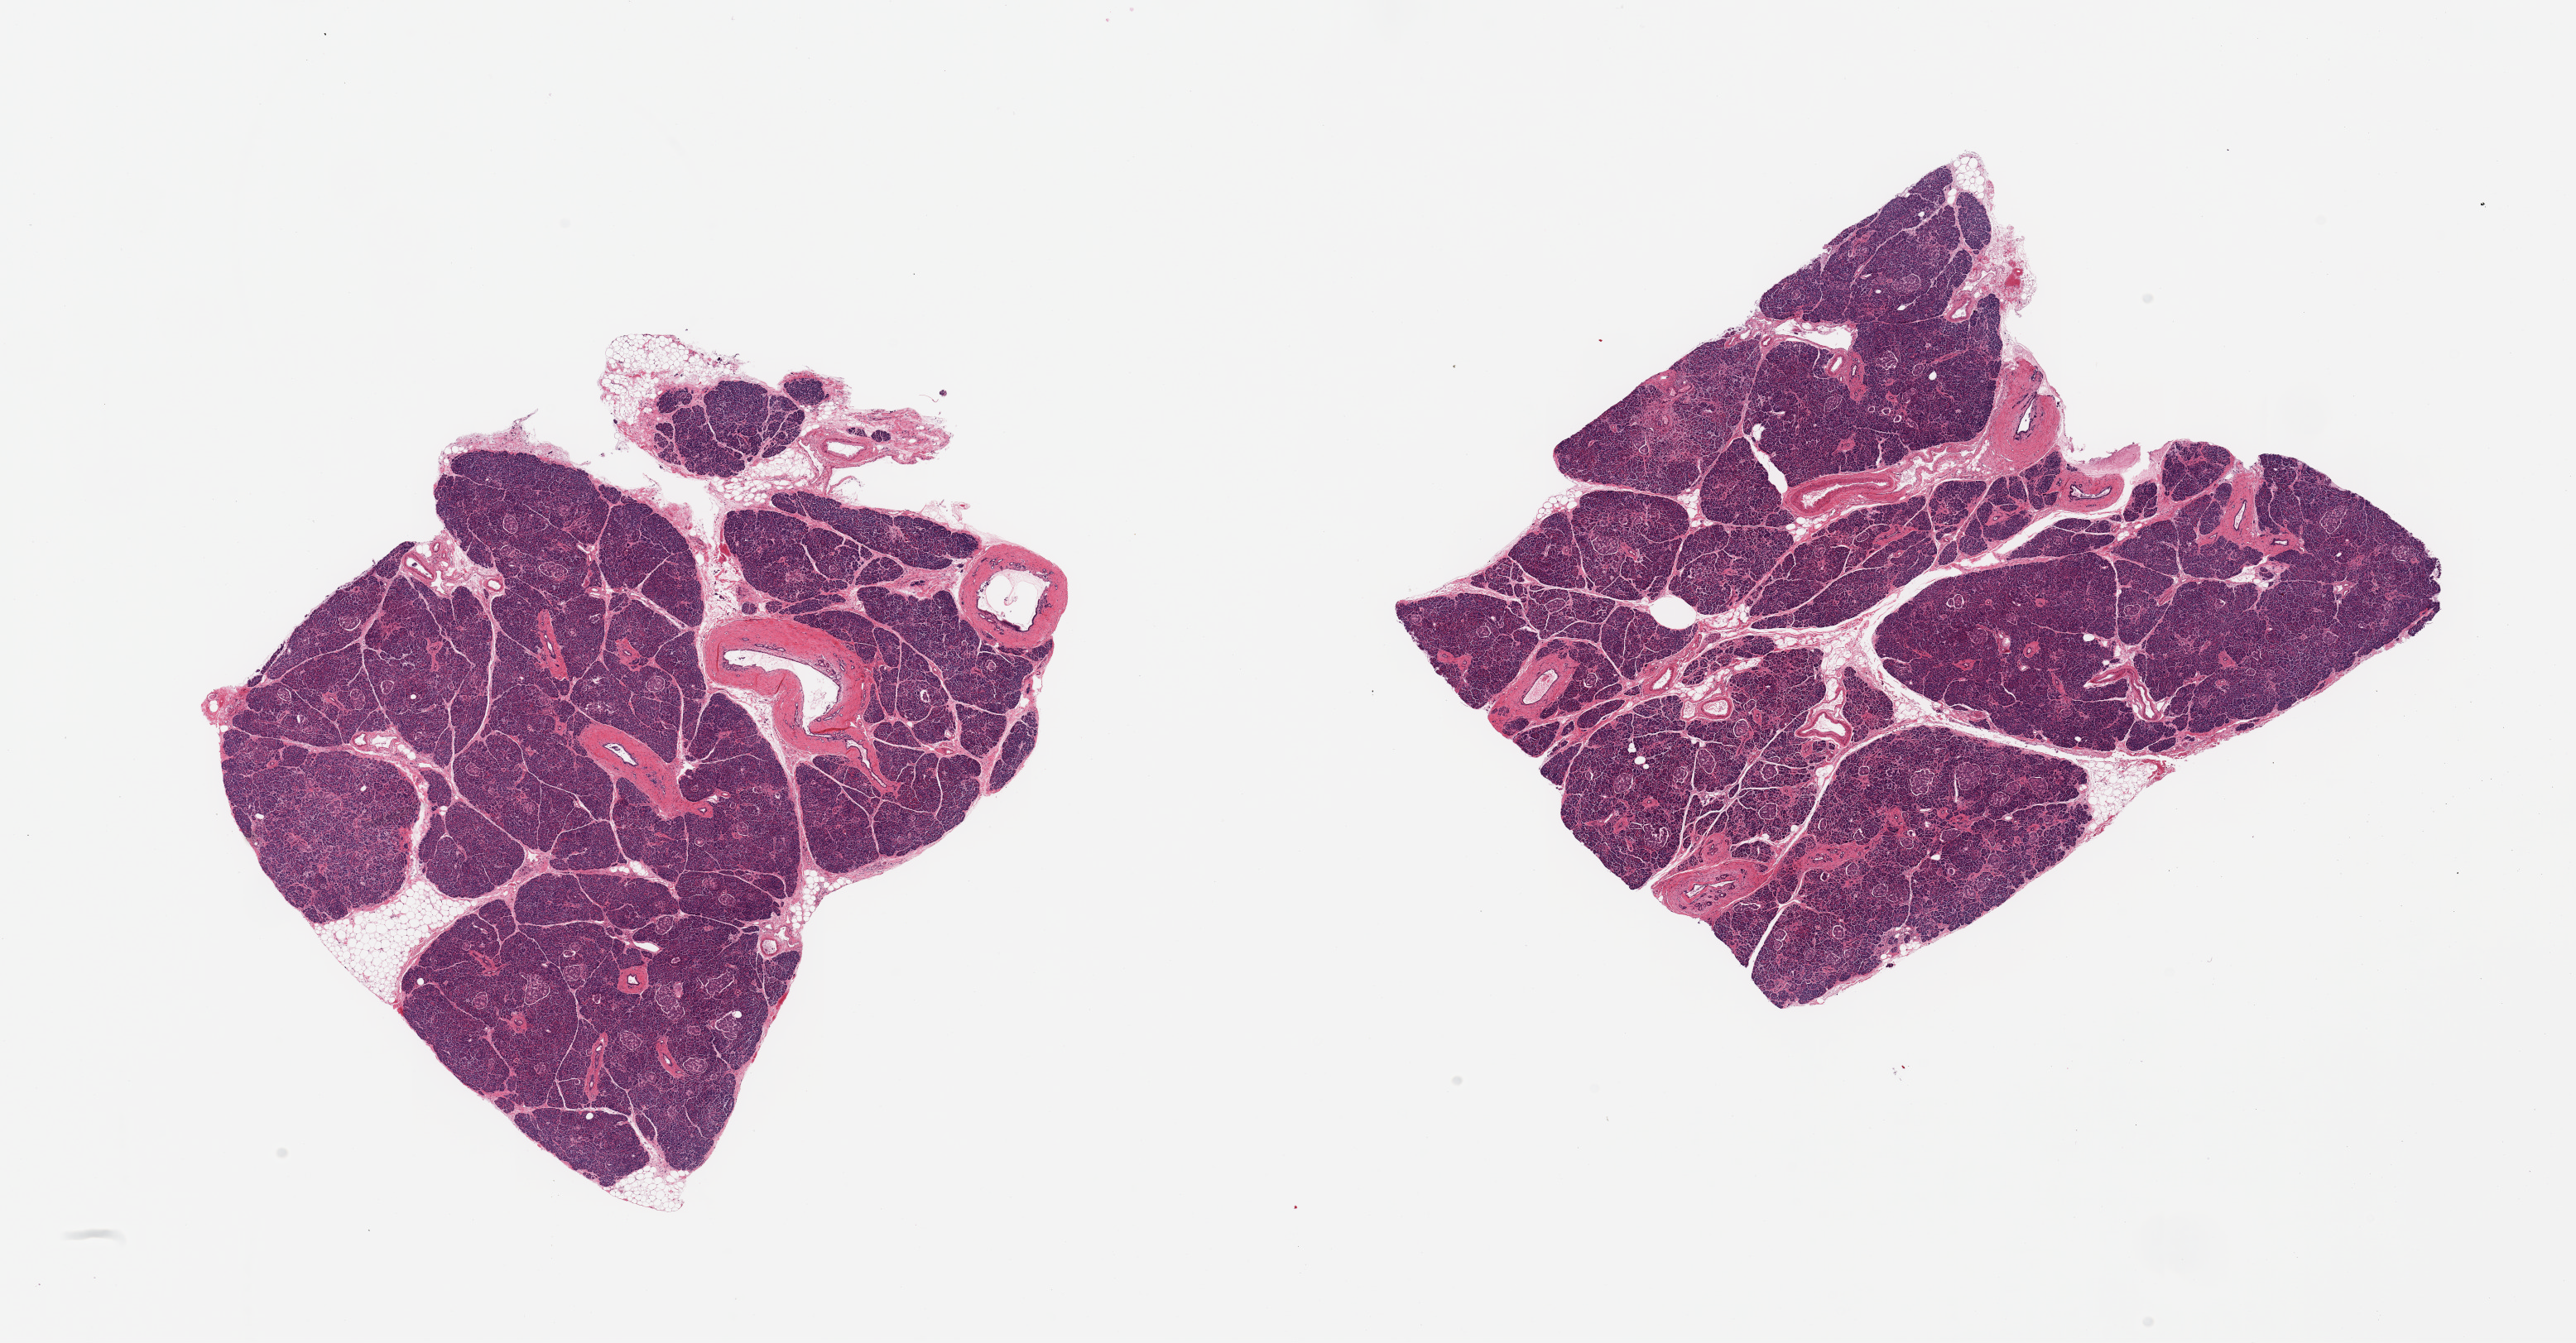
Digitized haematoxylin and eosin-stained section — a low-resolution overview of the entire scanned area, about 24.6 x 12.8 mm; PAXgene-fixed, paraffin-embedded tissue; sampled site (target tissue): pancreas; donor tissue sample. Donor: male.
* pathologist's review note for this sample: 2 pieces, Islets well preserved